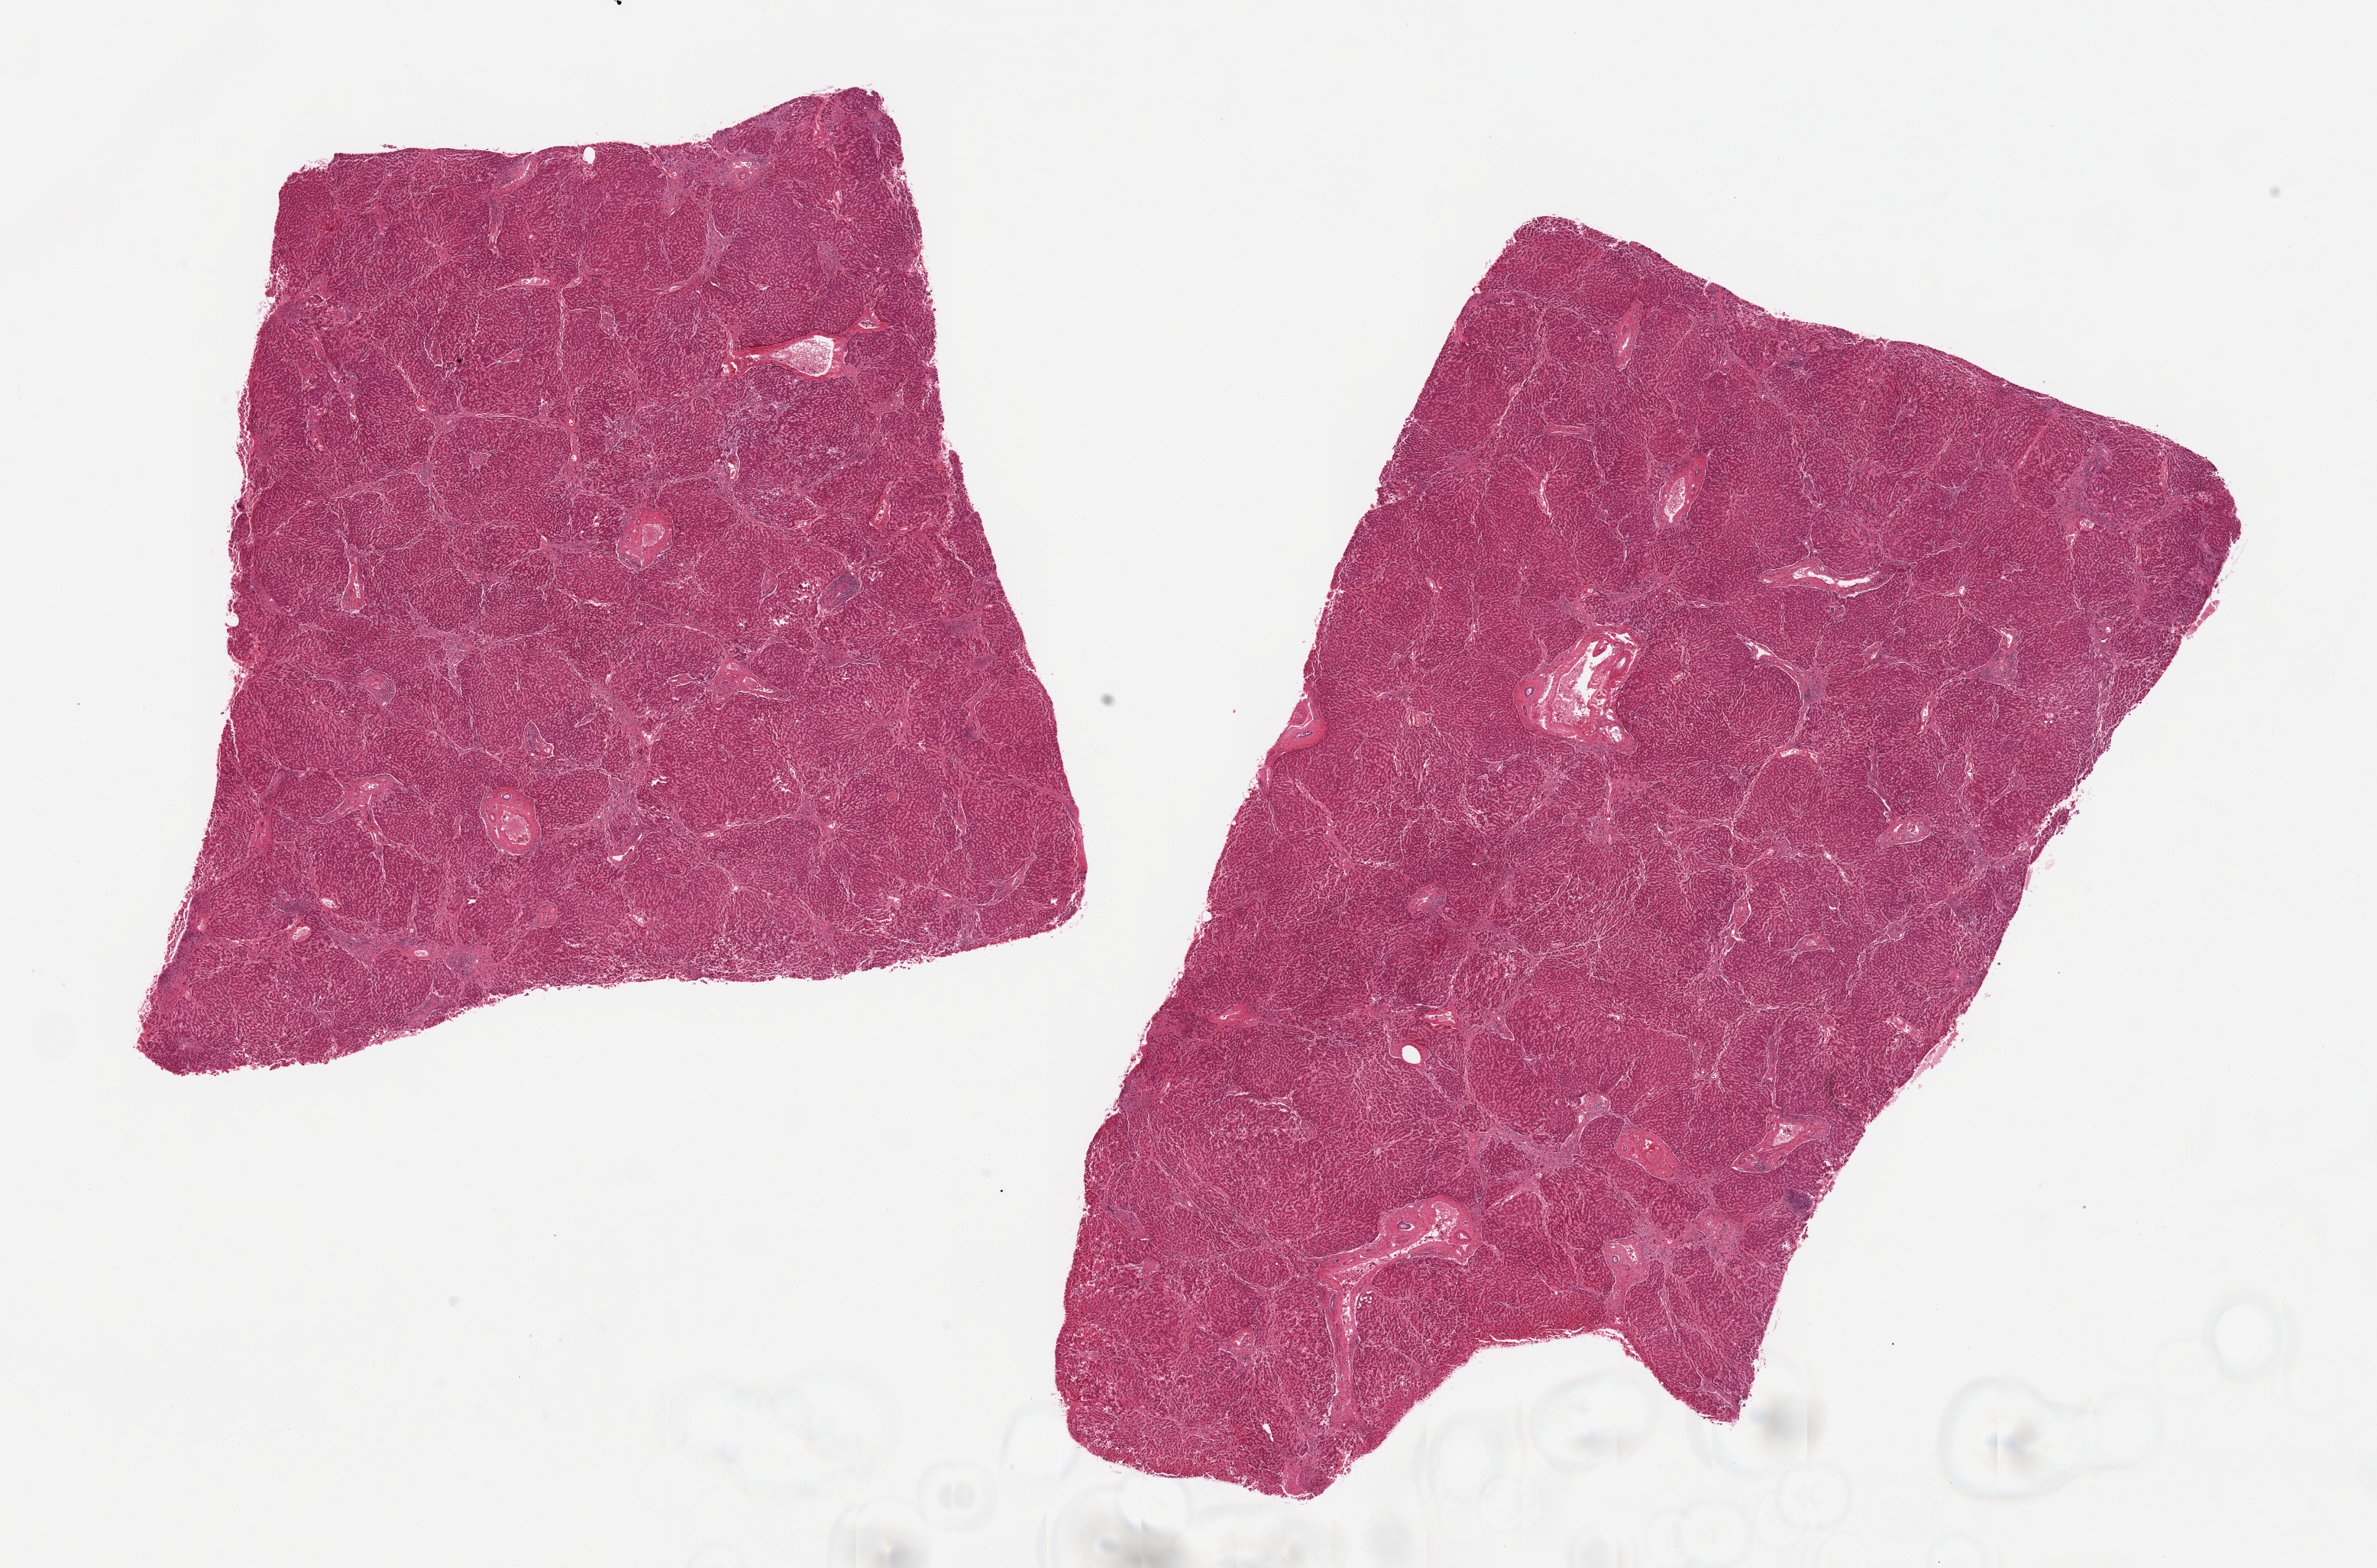
Digitized hematoxylin and eosin (H&E)-stained section, brightfield, a low-resolution overview of the entire scanned area, about 24.6 x 16.2 mm (acquisition: 20x scan). PAXgene-fixed paraffin-embedded (PFPE) section. Target tissue: liver. Tissue donor sample.
- pathologist's review note for this sample: 2 pieces, mild steatosis, widening of sinusoids with bridging fibrosis, chronic inflammation